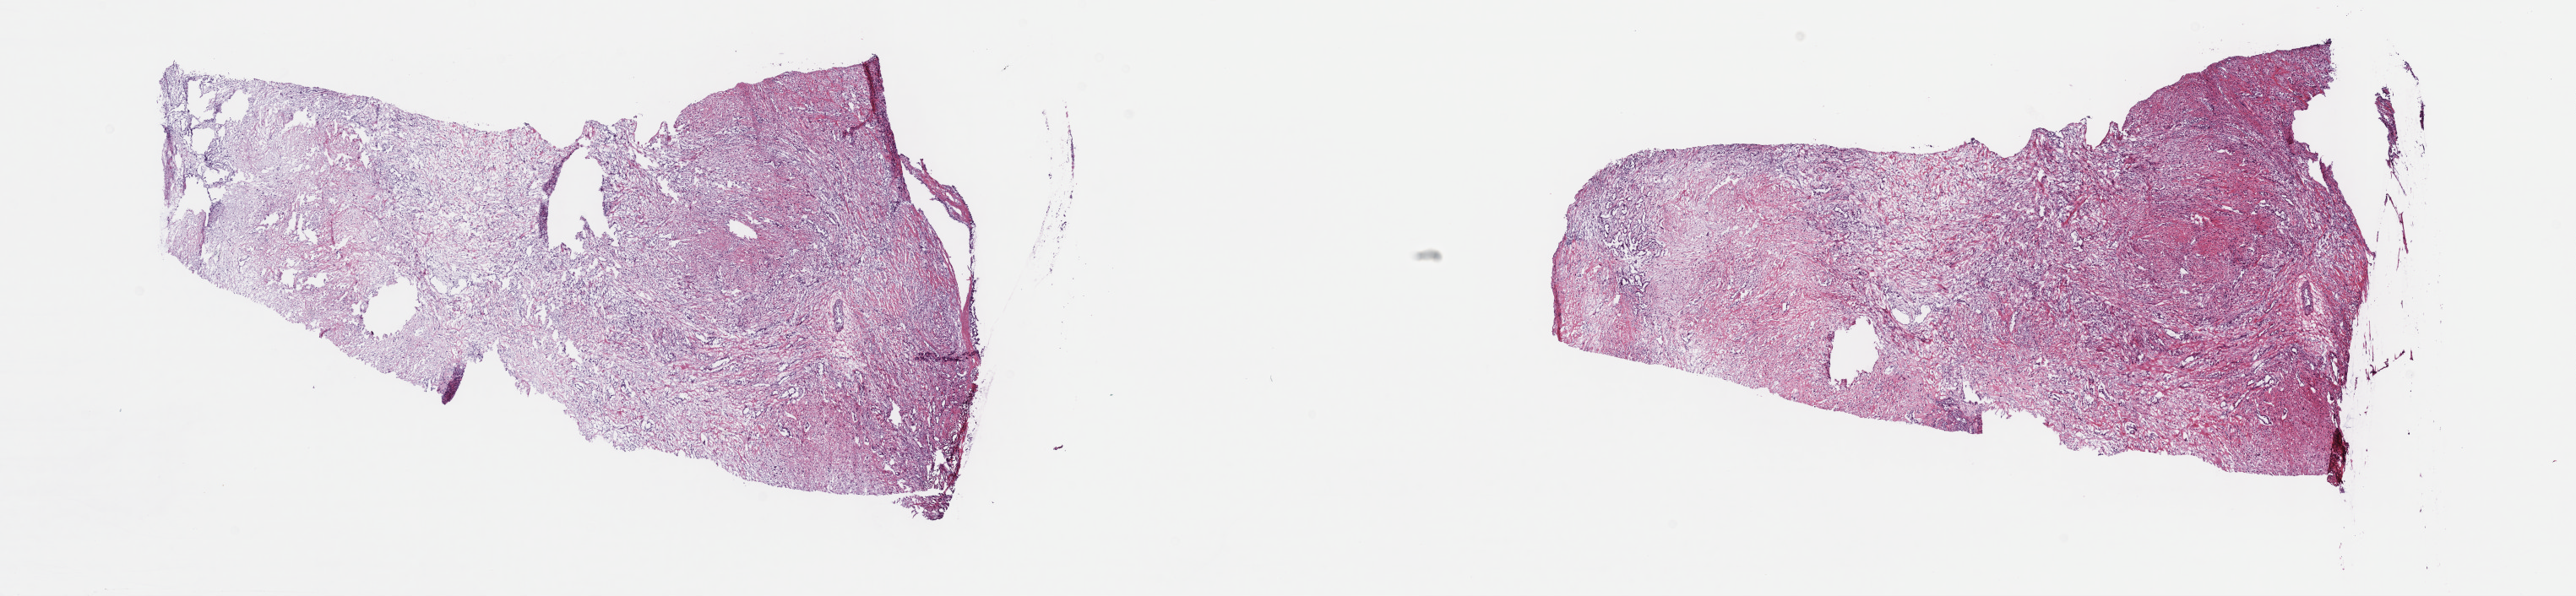
Whole-slide histology image, Hematoxylin and eosin (H&E) stained, shown as a low-resolution overview of the whole scanned area (about 24.7 x 5.7 mm, from a 40x scan), frozen section from the top of the tissue portion, sample: primary tumour, mesothelium. Male patient; age at initial diagnosis 80 years. Pathologist review of this section (percent, as recorded): tumour cells 100%, tumour nuclei 80%.
Histologic diagnosis: Mesothelioma, biphasic, malignant (pleura, NOS).